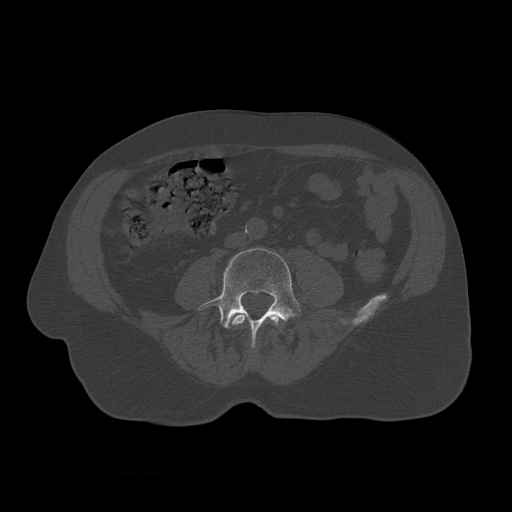
CT including the spine, one axial slice; position 281 of 450 along the scan axis; reconstruction kernel STANDARD; 120 kVp; bone window (W 1800 / L 400 HU); 512 × 512 image matrix, field of view 405 × 405 mm. Patient age 75 years. From the clinical record (not read from this slice): primary cancer: prostate.
Structures marked on this image (semi-automatically segmented with operator editing):
- L3 vertebra: bounding box <230,313,281,353> (left, top, right, bottom; pixels)
- L4 vertebra: <198,248,301,347>